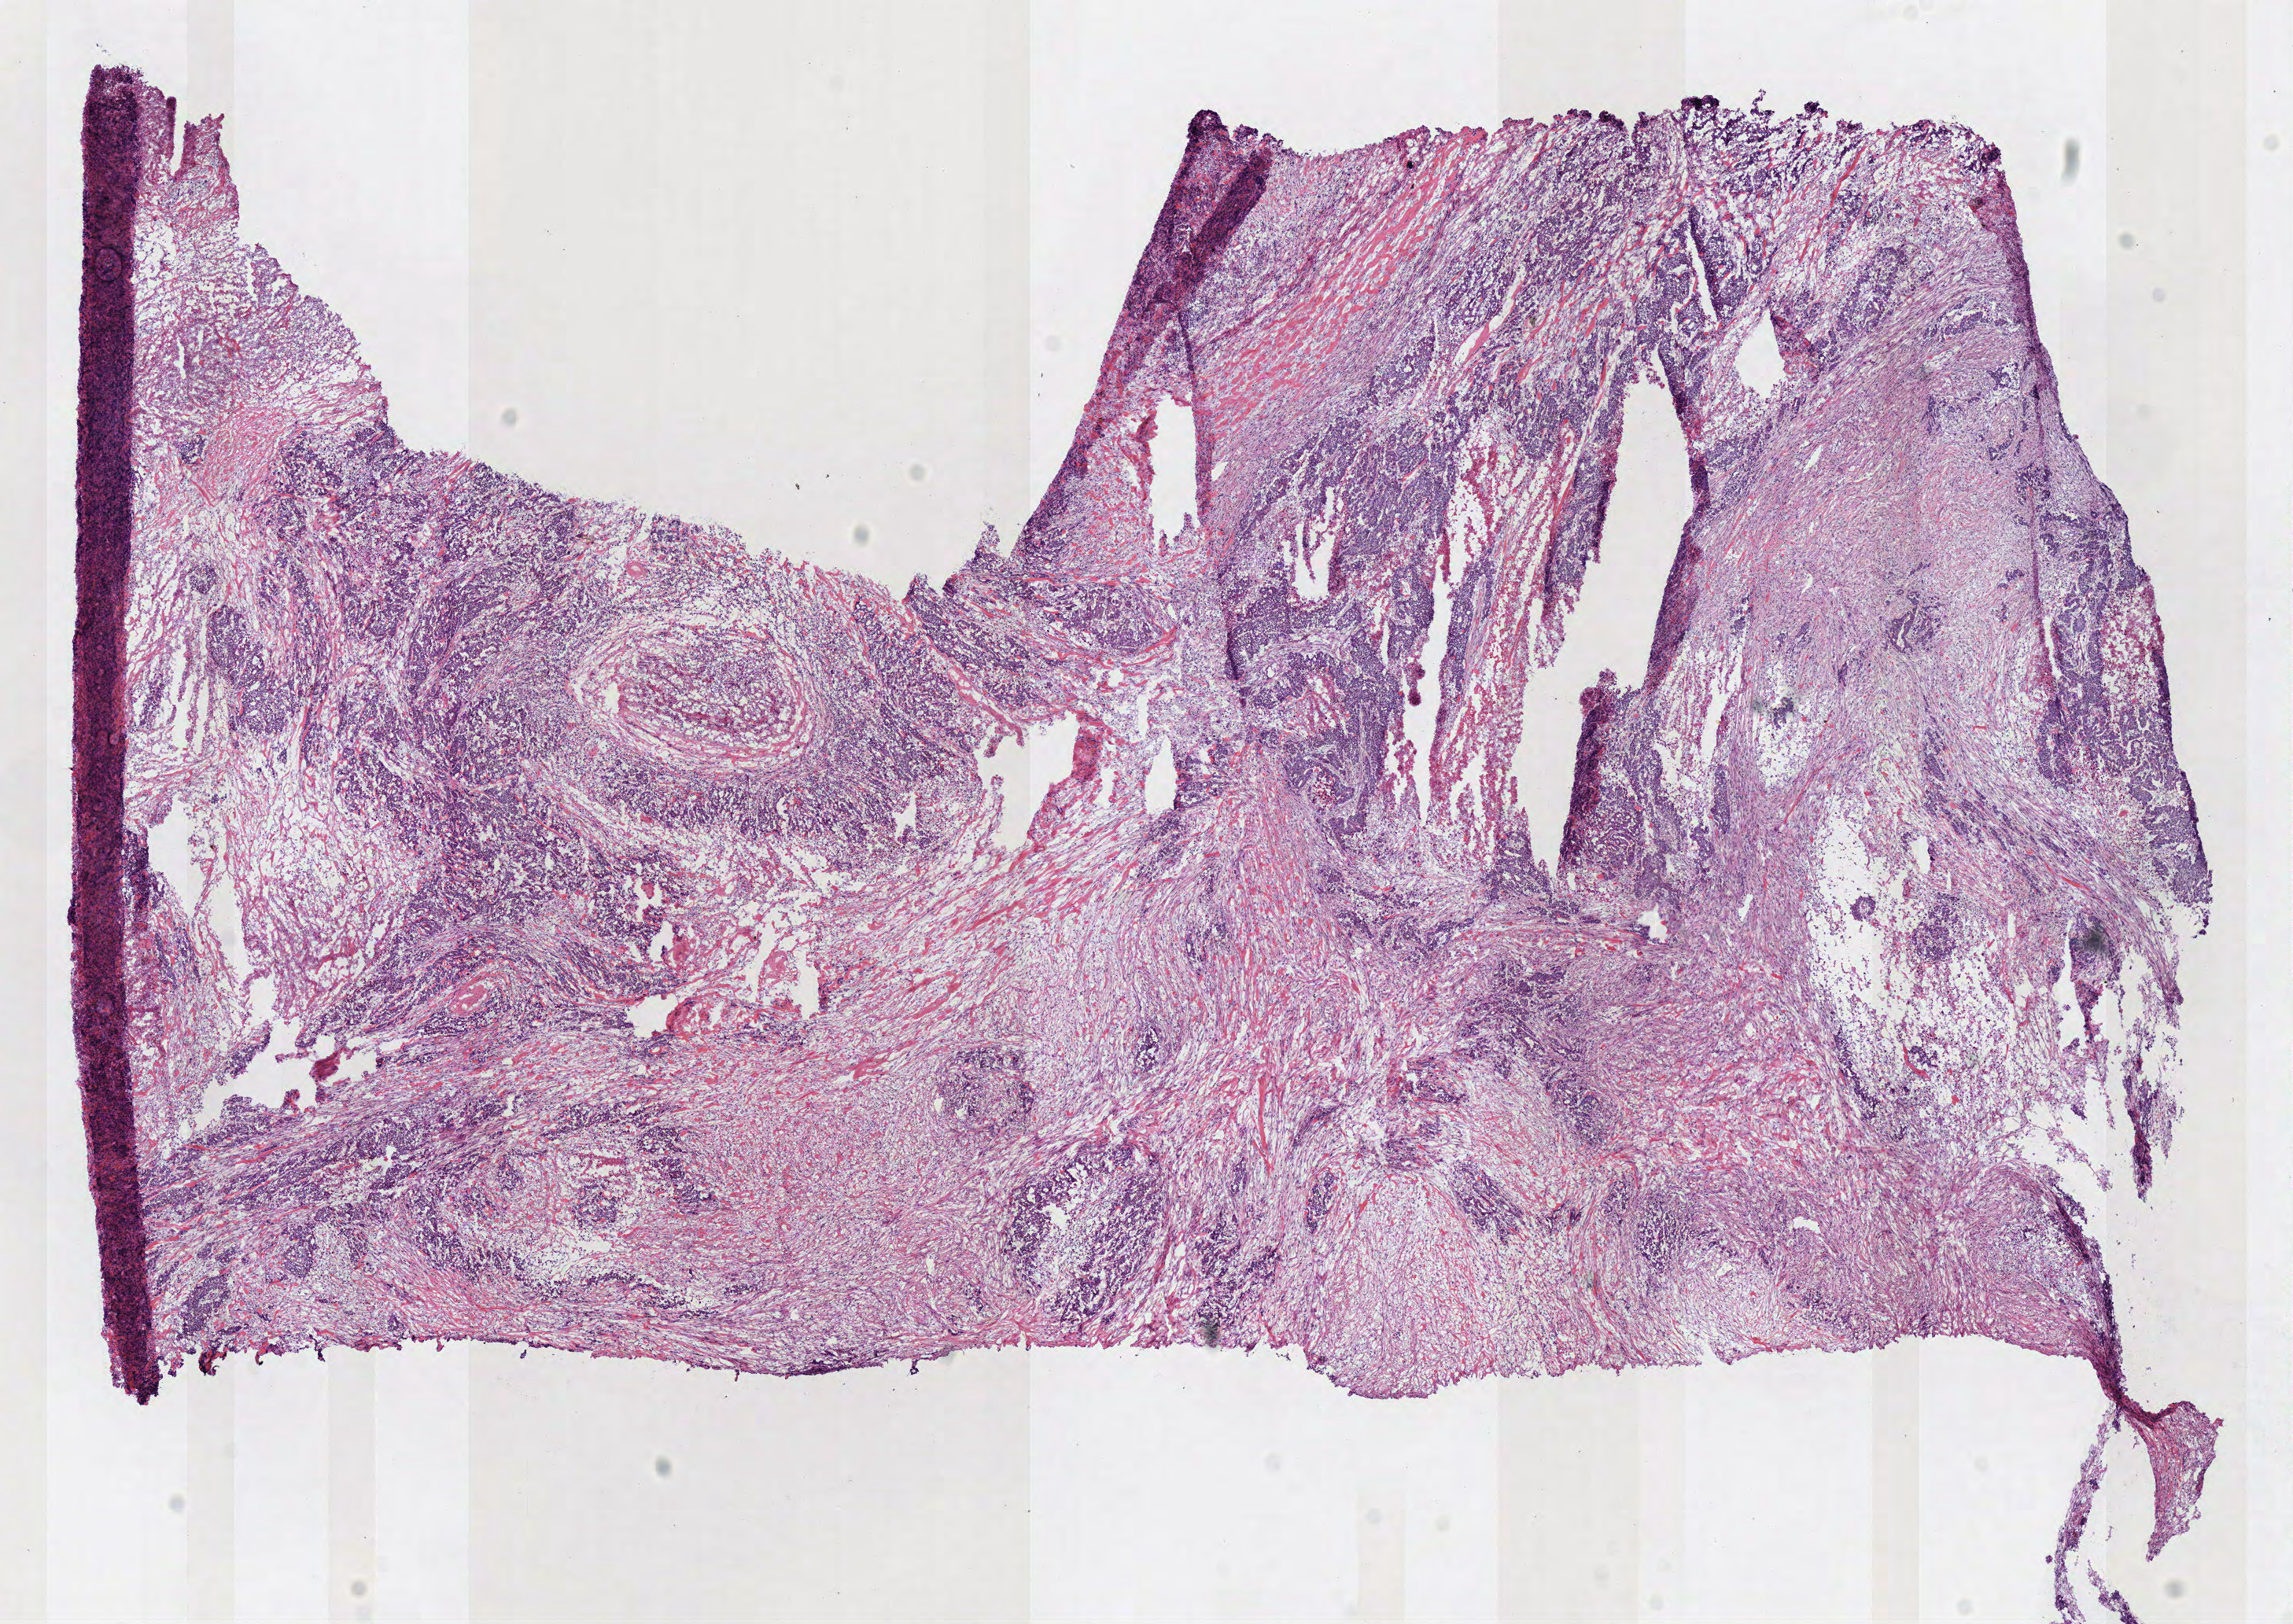
Digitized H&E tissue section (whole slide), a low-resolution overview of the entire scanned area, about 11.5 x 8.1 mm (from a 40x scan). Frozen section from the bottom of the tissue portion. Sample: primary tumour, rectum. Male patient; age at initial diagnosis 33 years. Composition of this section per pathologist review: tumour cells 30%, tumour nuclei 50%, normal cells 0%, stromal cells 52%, necrosis 18%. Inflammatory infiltration, as recorded: lymphocyte infiltration 10%.
• TNM: T3 N1 M0
• lymph nodes positive (case pathology): 3 of 14 examined
• AJCC pathologic stage: IIIA (7th edition)
• diagnosis: Adenocarcinoma with mixed subtypes